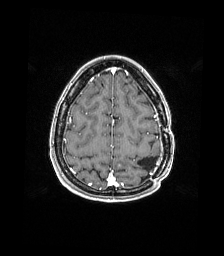
Brain MRI from a brain-tumour surgery series, one axial slice. Position 46 of 176 along the scan axis. T1-weighted post-contrast. 1 mm slice thickness. 224 × 256 image matrix, field of view 224 × 256 mm. Case-level facts recorded for this patient, not image findings: histopathology: Atypical meningioma; WHO grade: 2; tumour location: Paramedian Left Parietal.
Annotated regions visible in this slice (outlined manually by an expert reader):
- previous resection cavity: bounding box [x1, y1, x2, y2] px = [138, 157, 157, 170]
- tumour: [118, 164, 121, 166]